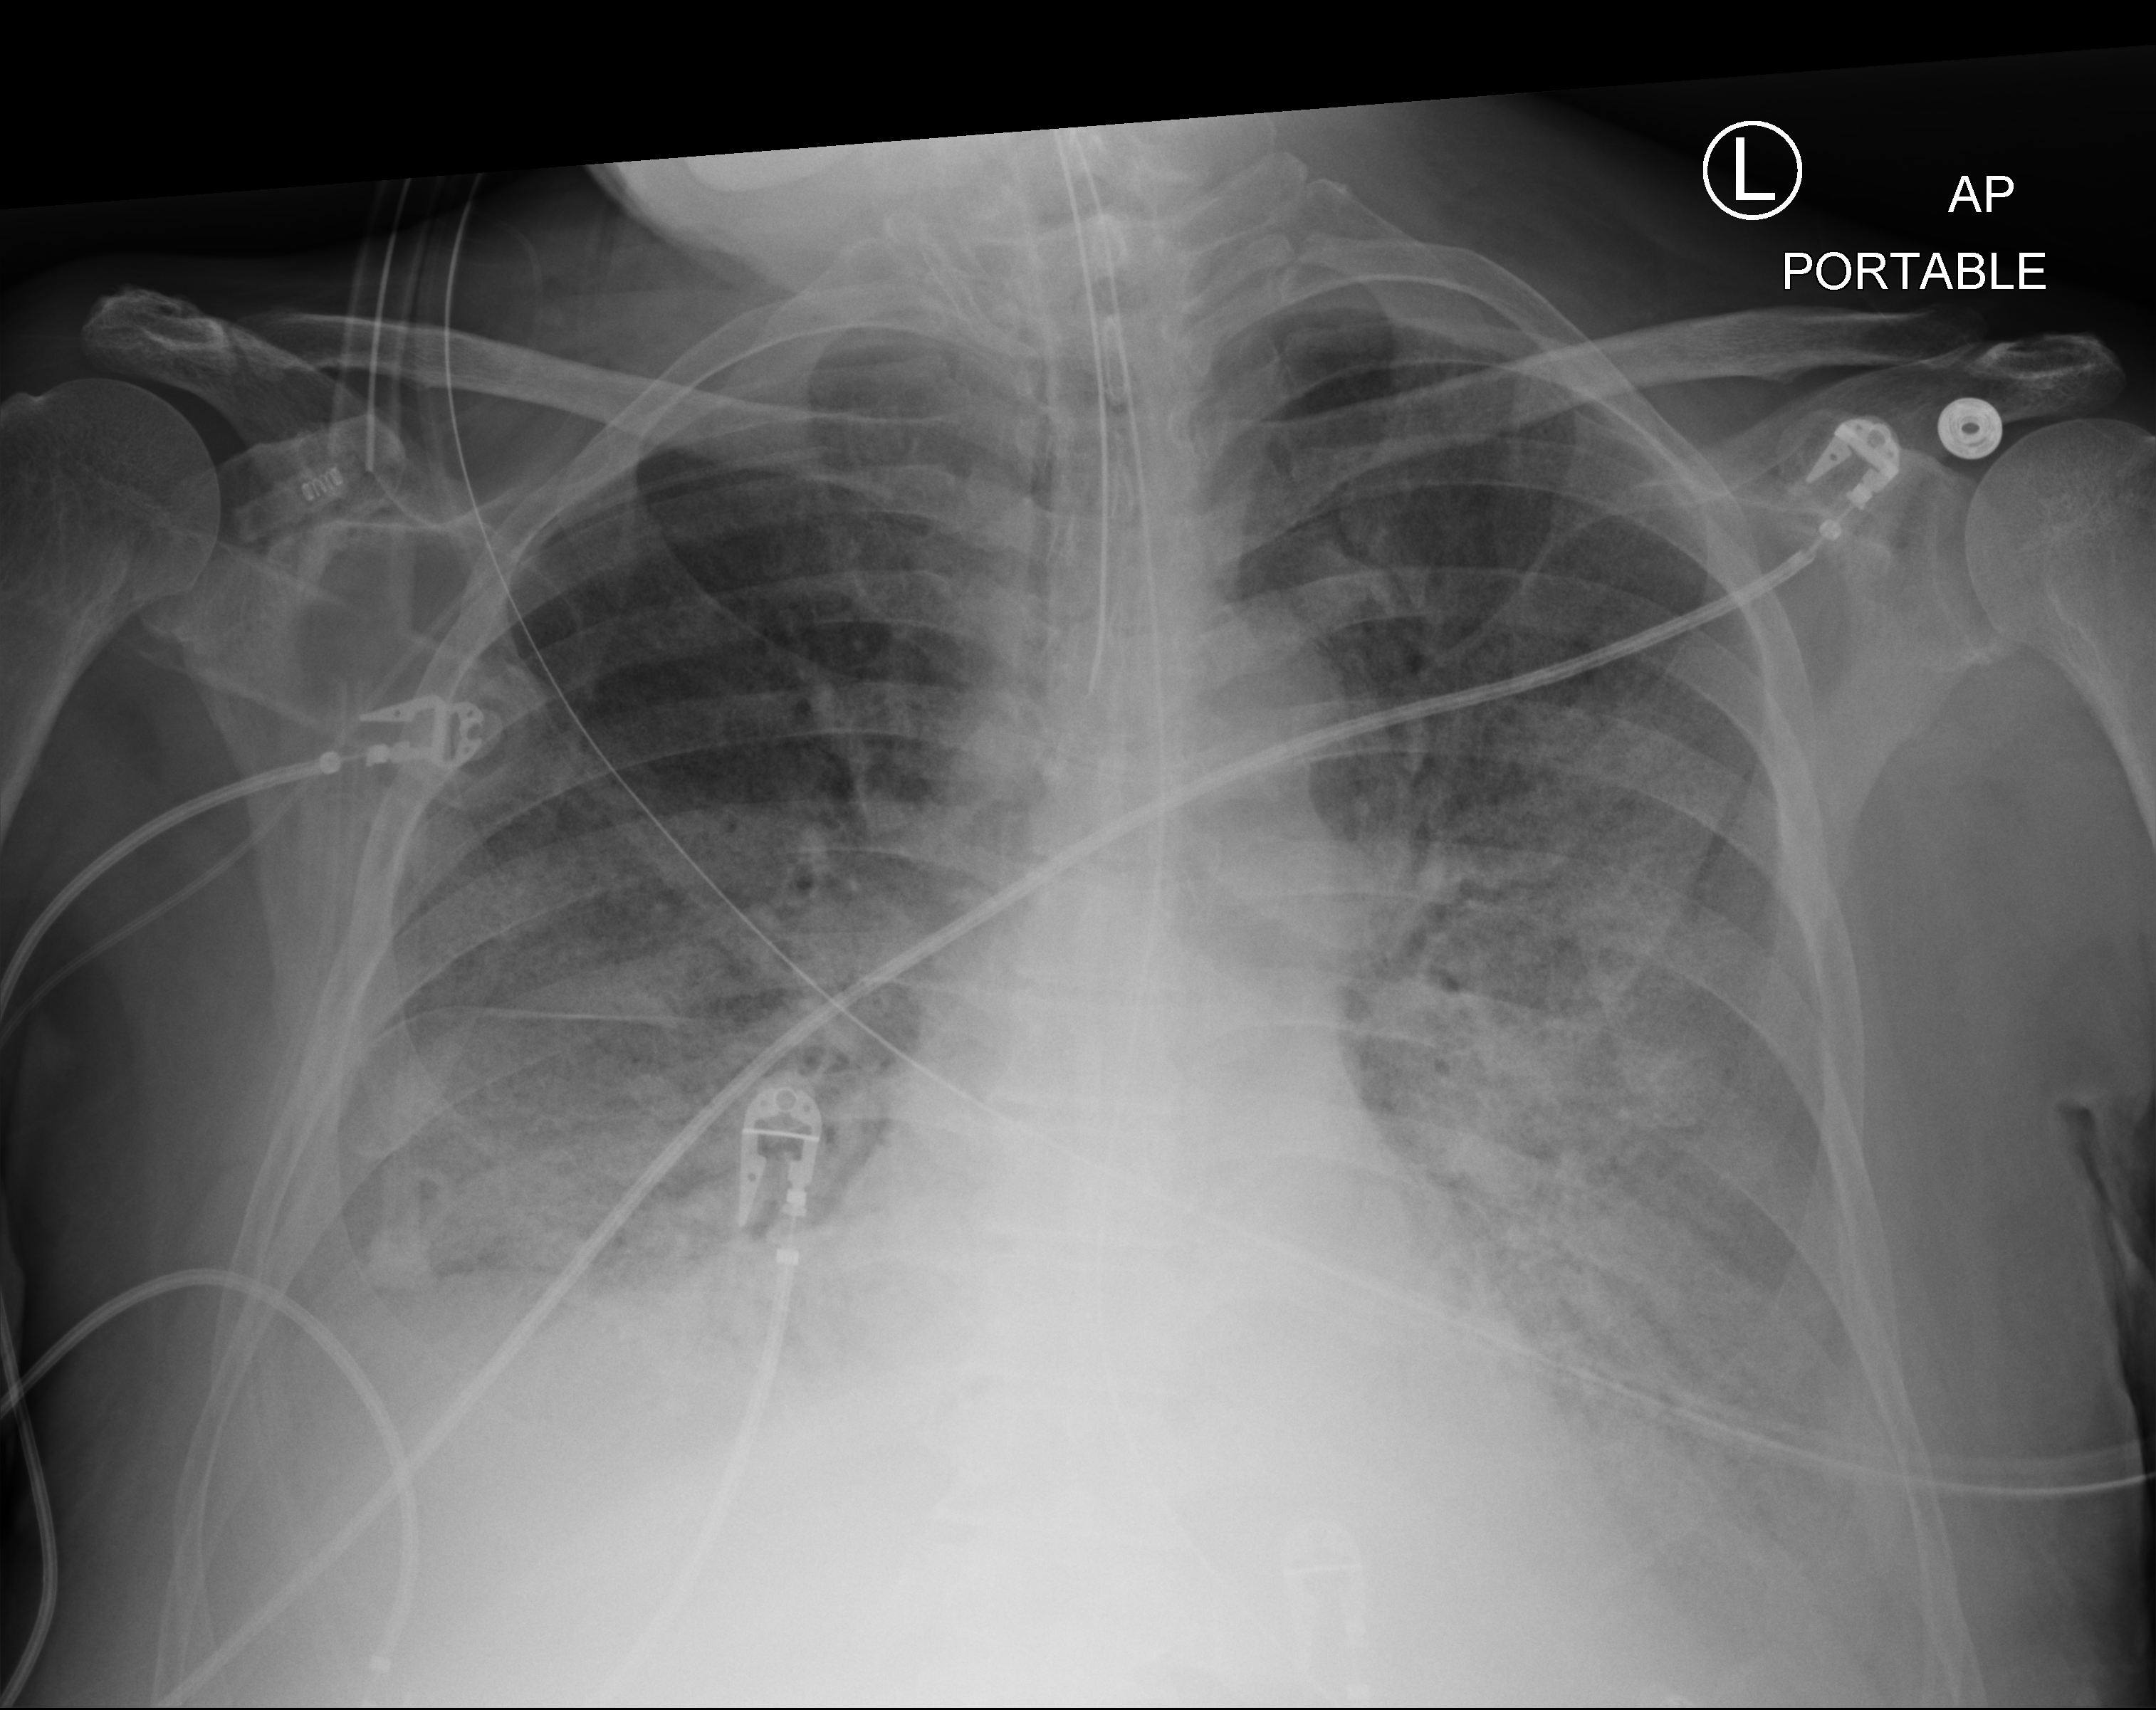
Bedside chest radiograph (computed radiography); anteroposterior (AP) projection. Patient hospitalised with COVID-19; male, aged 60–74 years.
Admission-level facts for this patient (not findings on this image; timing relative to this image not recorded): mechanically ventilated during this hospital stay: yes; admitted to intensive care during this hospital stay: yes.